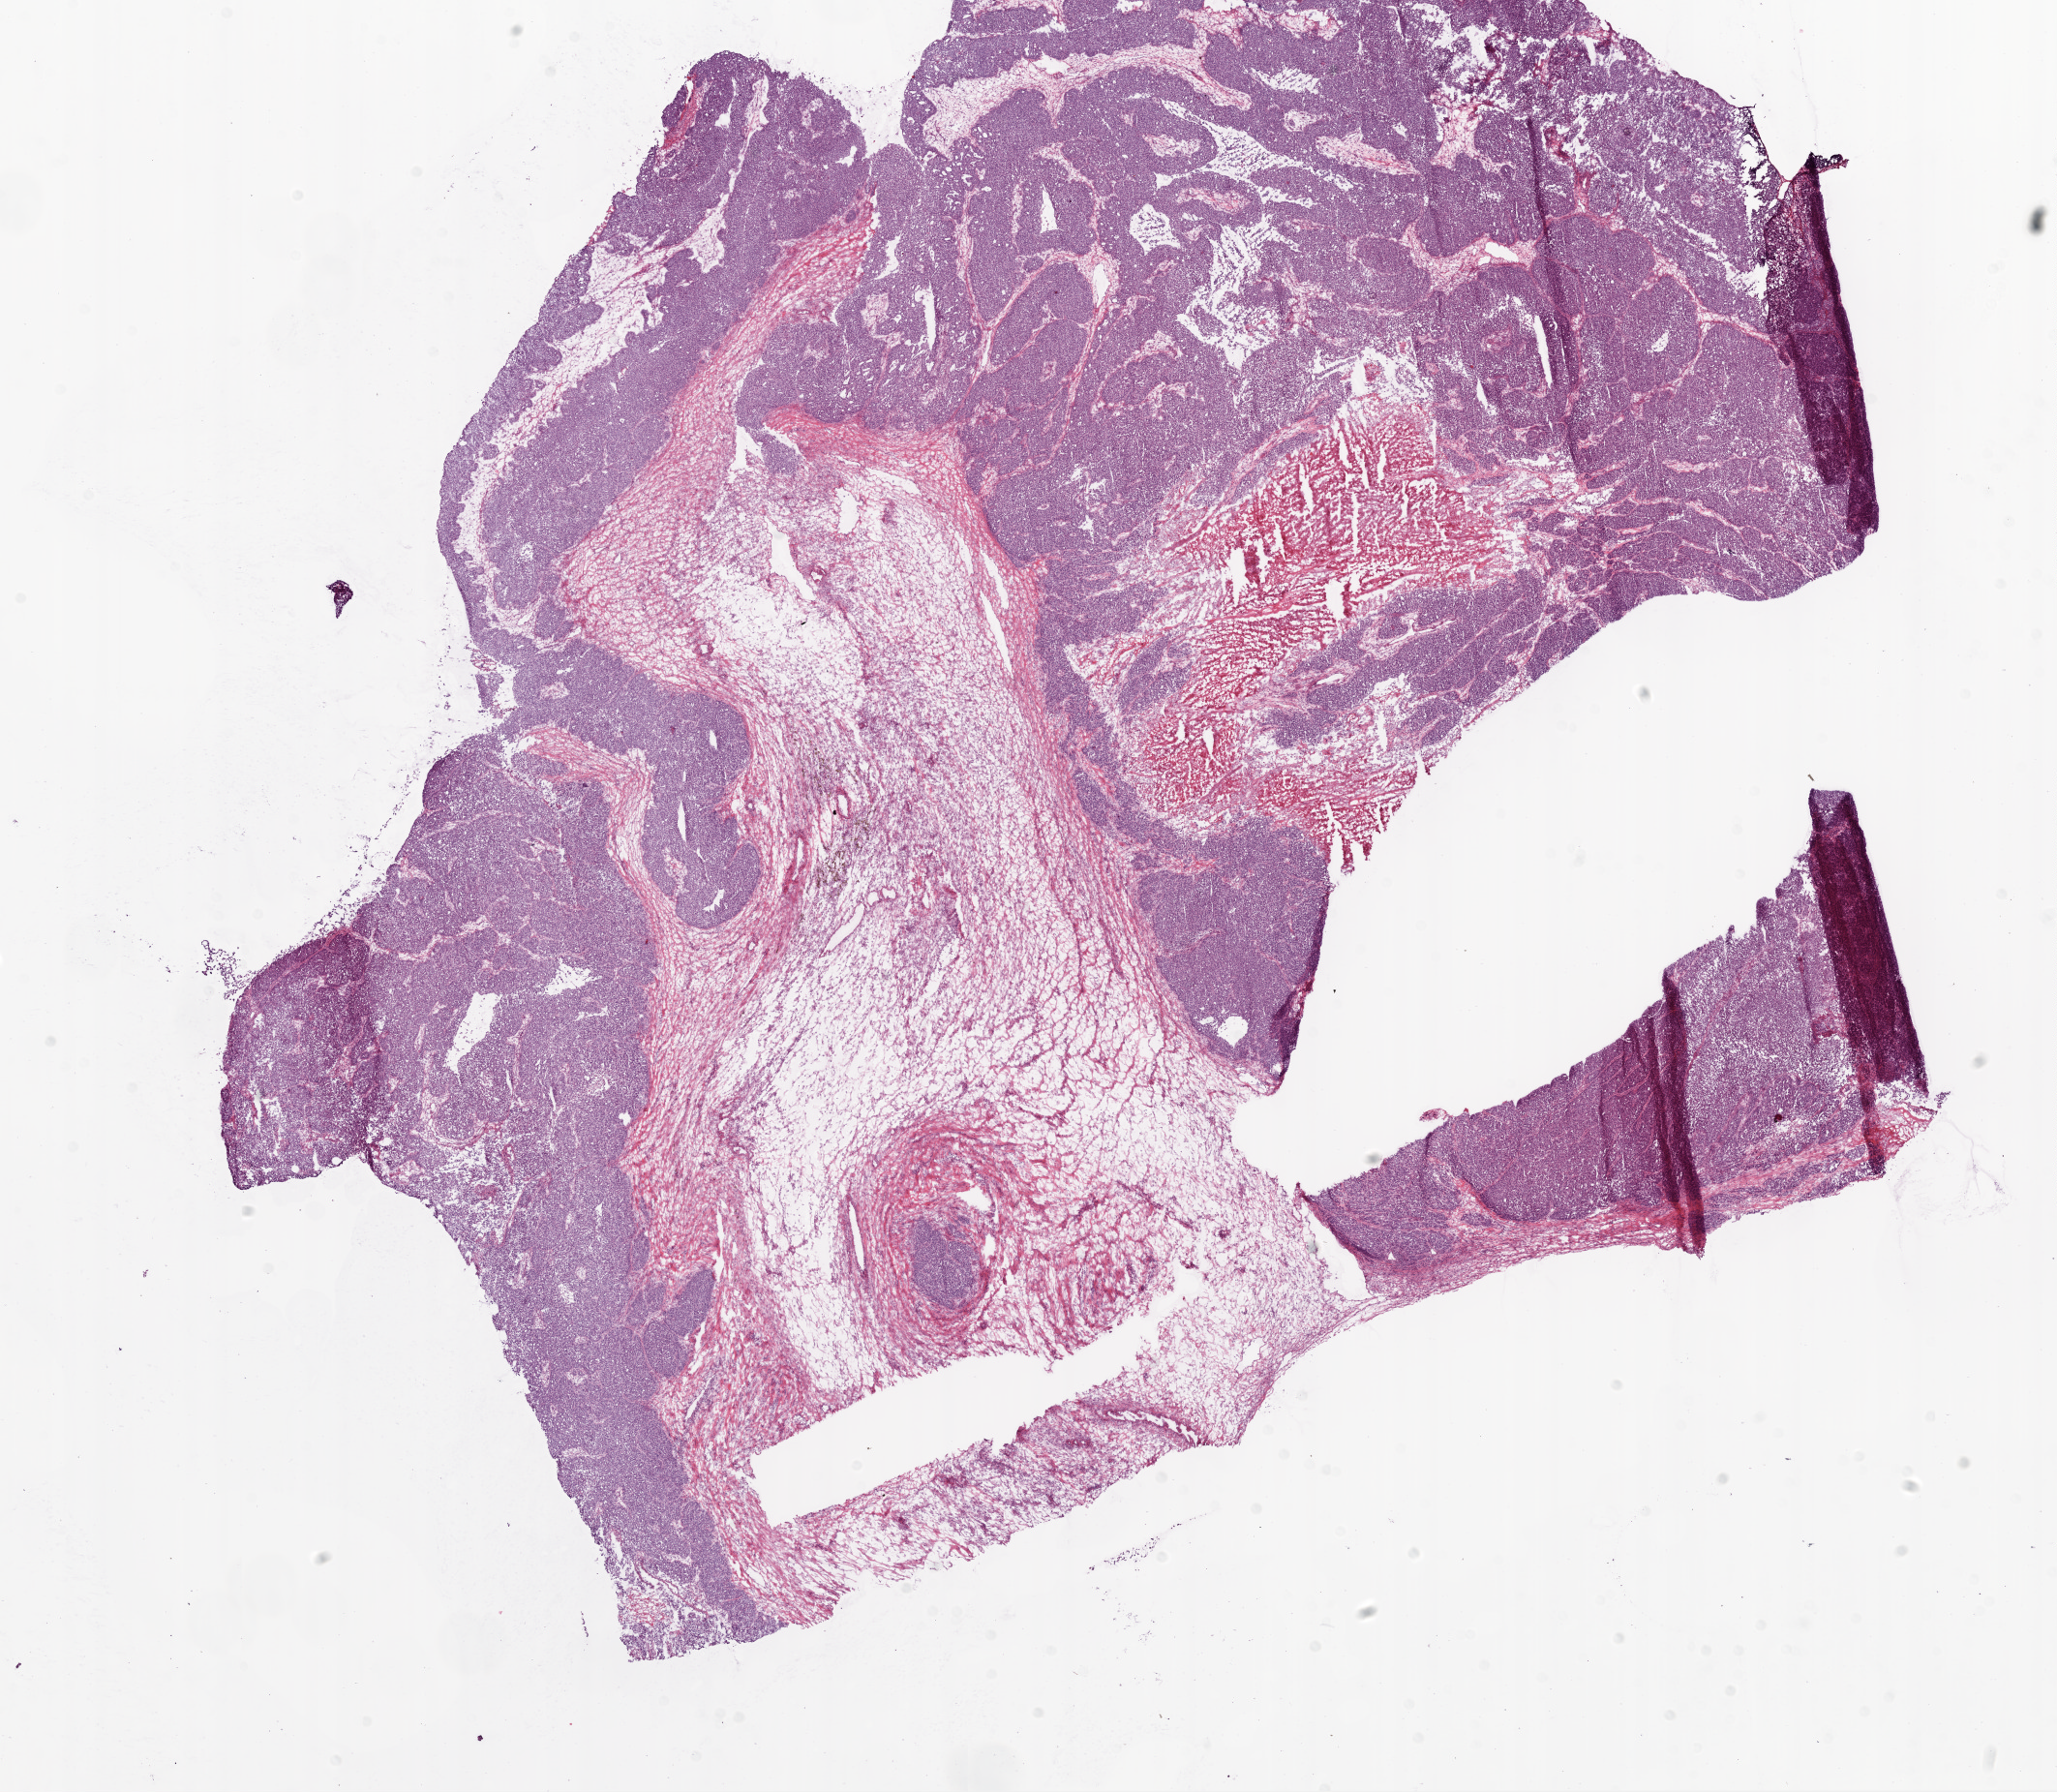
Whole-slide histology image, H&E-stained — low-resolution overview of the scanned area, about 17.1 x 14.9 mm (acquisition: 20x scan), frozen section from the bottom of the tissue portion, ovary, primary tumour sample. Female patient; age at initial diagnosis 45 years.
Pathologic diagnosis: Serous cystadenocarcinoma, NOS.